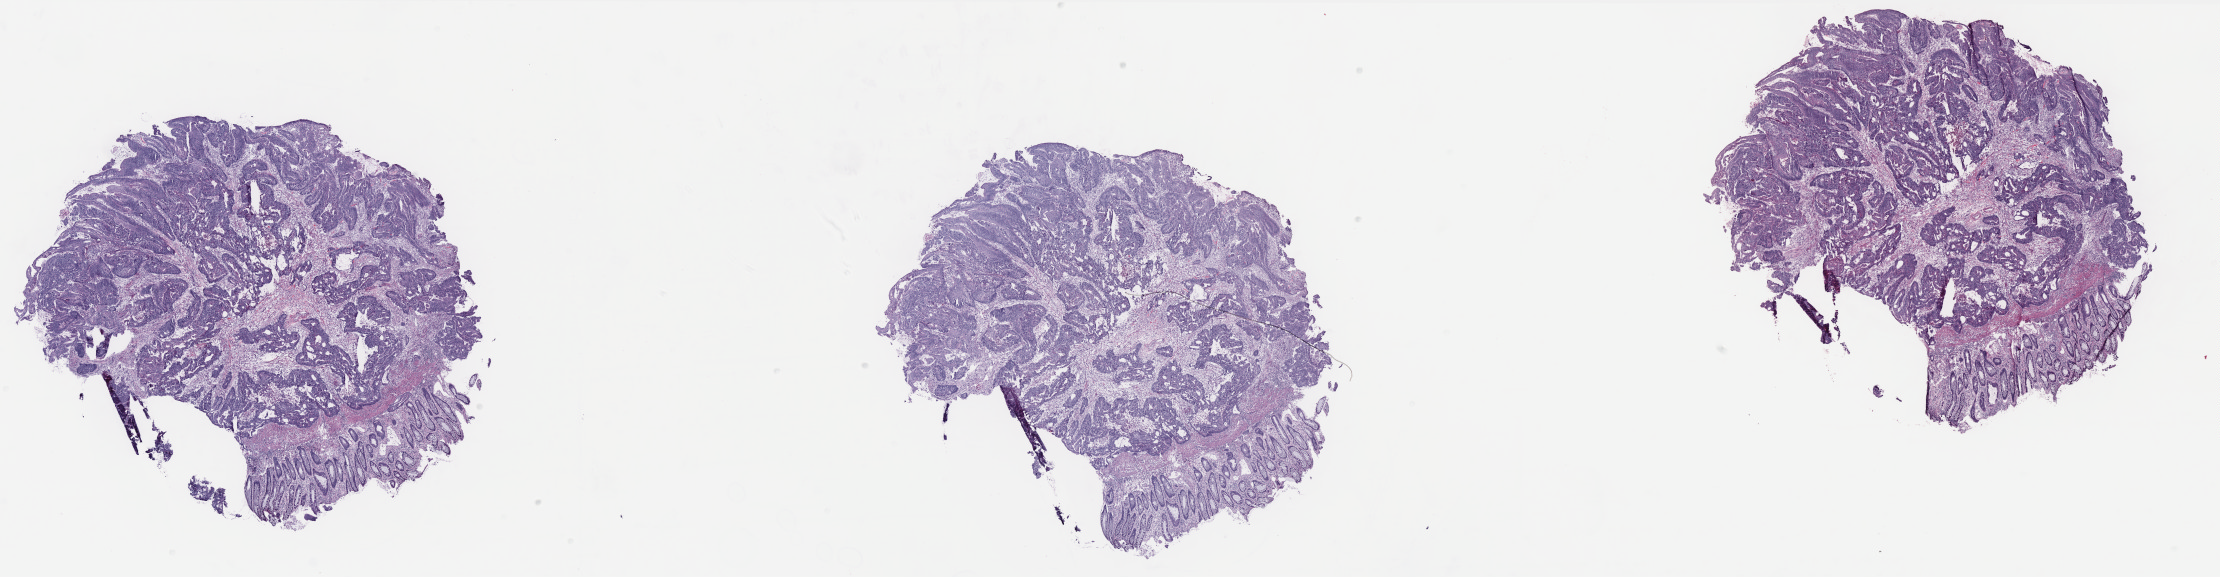
H&E-stained whole-slide image — shown as a low-resolution overview of the whole scanned area (about 35.6 x 9.3 mm, from a 40x scan); frozen section from the bottom of the tissue portion; rectum, primary tumour sample. Male, age 58 years at initial diagnosis. Slide review estimates, as recorded: tumour cells 84%, tumour nuclei 75%, normal cells 15%, stromal cells 0%, necrosis 1%. Infiltration values recorded for this section: lymphocyte infiltration 3%, monocyte infiltration 2%, neutrophil infiltration 3%.
• TNM: T3 N1 M0
• lymph nodes positive (case pathology): 2 of 47 examined
• AJCC pathologic stage: IIIB (6th edition)
• histologic diagnosis: Adenocarcinoma, NOS